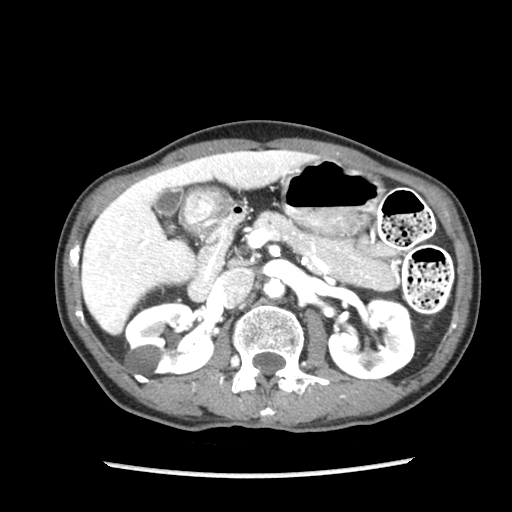
Contrast-enhanced abdominal CT (liver protocol), one axial slice. Position 45 of 87 along the scan axis. Reconstruction kernel STANDARD. Soft-tissue window (W 400 / L 40 HU). 2.5 mm slice thickness. 512 × 512 image matrix, field of view 300 × 300 mm. Case-level facts recorded for this patient, not image findings: diagnosis: hepatocellular carcinoma (patient treated with transarterial chemoembolisation; whether this scan precedes or follows treatment is not stated here); TNM stage (as recorded): Stage-IIIB; Child-Pugh class: A; tumour differentiation: well differentiated; tumour nodularity: uninodular.
Outlined on this slice (semi-automatic segmentation, software-assisted and operator-edited):
- liver parenchyma outside the tumour (the mass and vessels are separate outlines, so this box may not span the whole liver): bounding box <82,150,319,334> (left, top, right, bottom; pixels)
- liver vessels: <85,171,192,322>